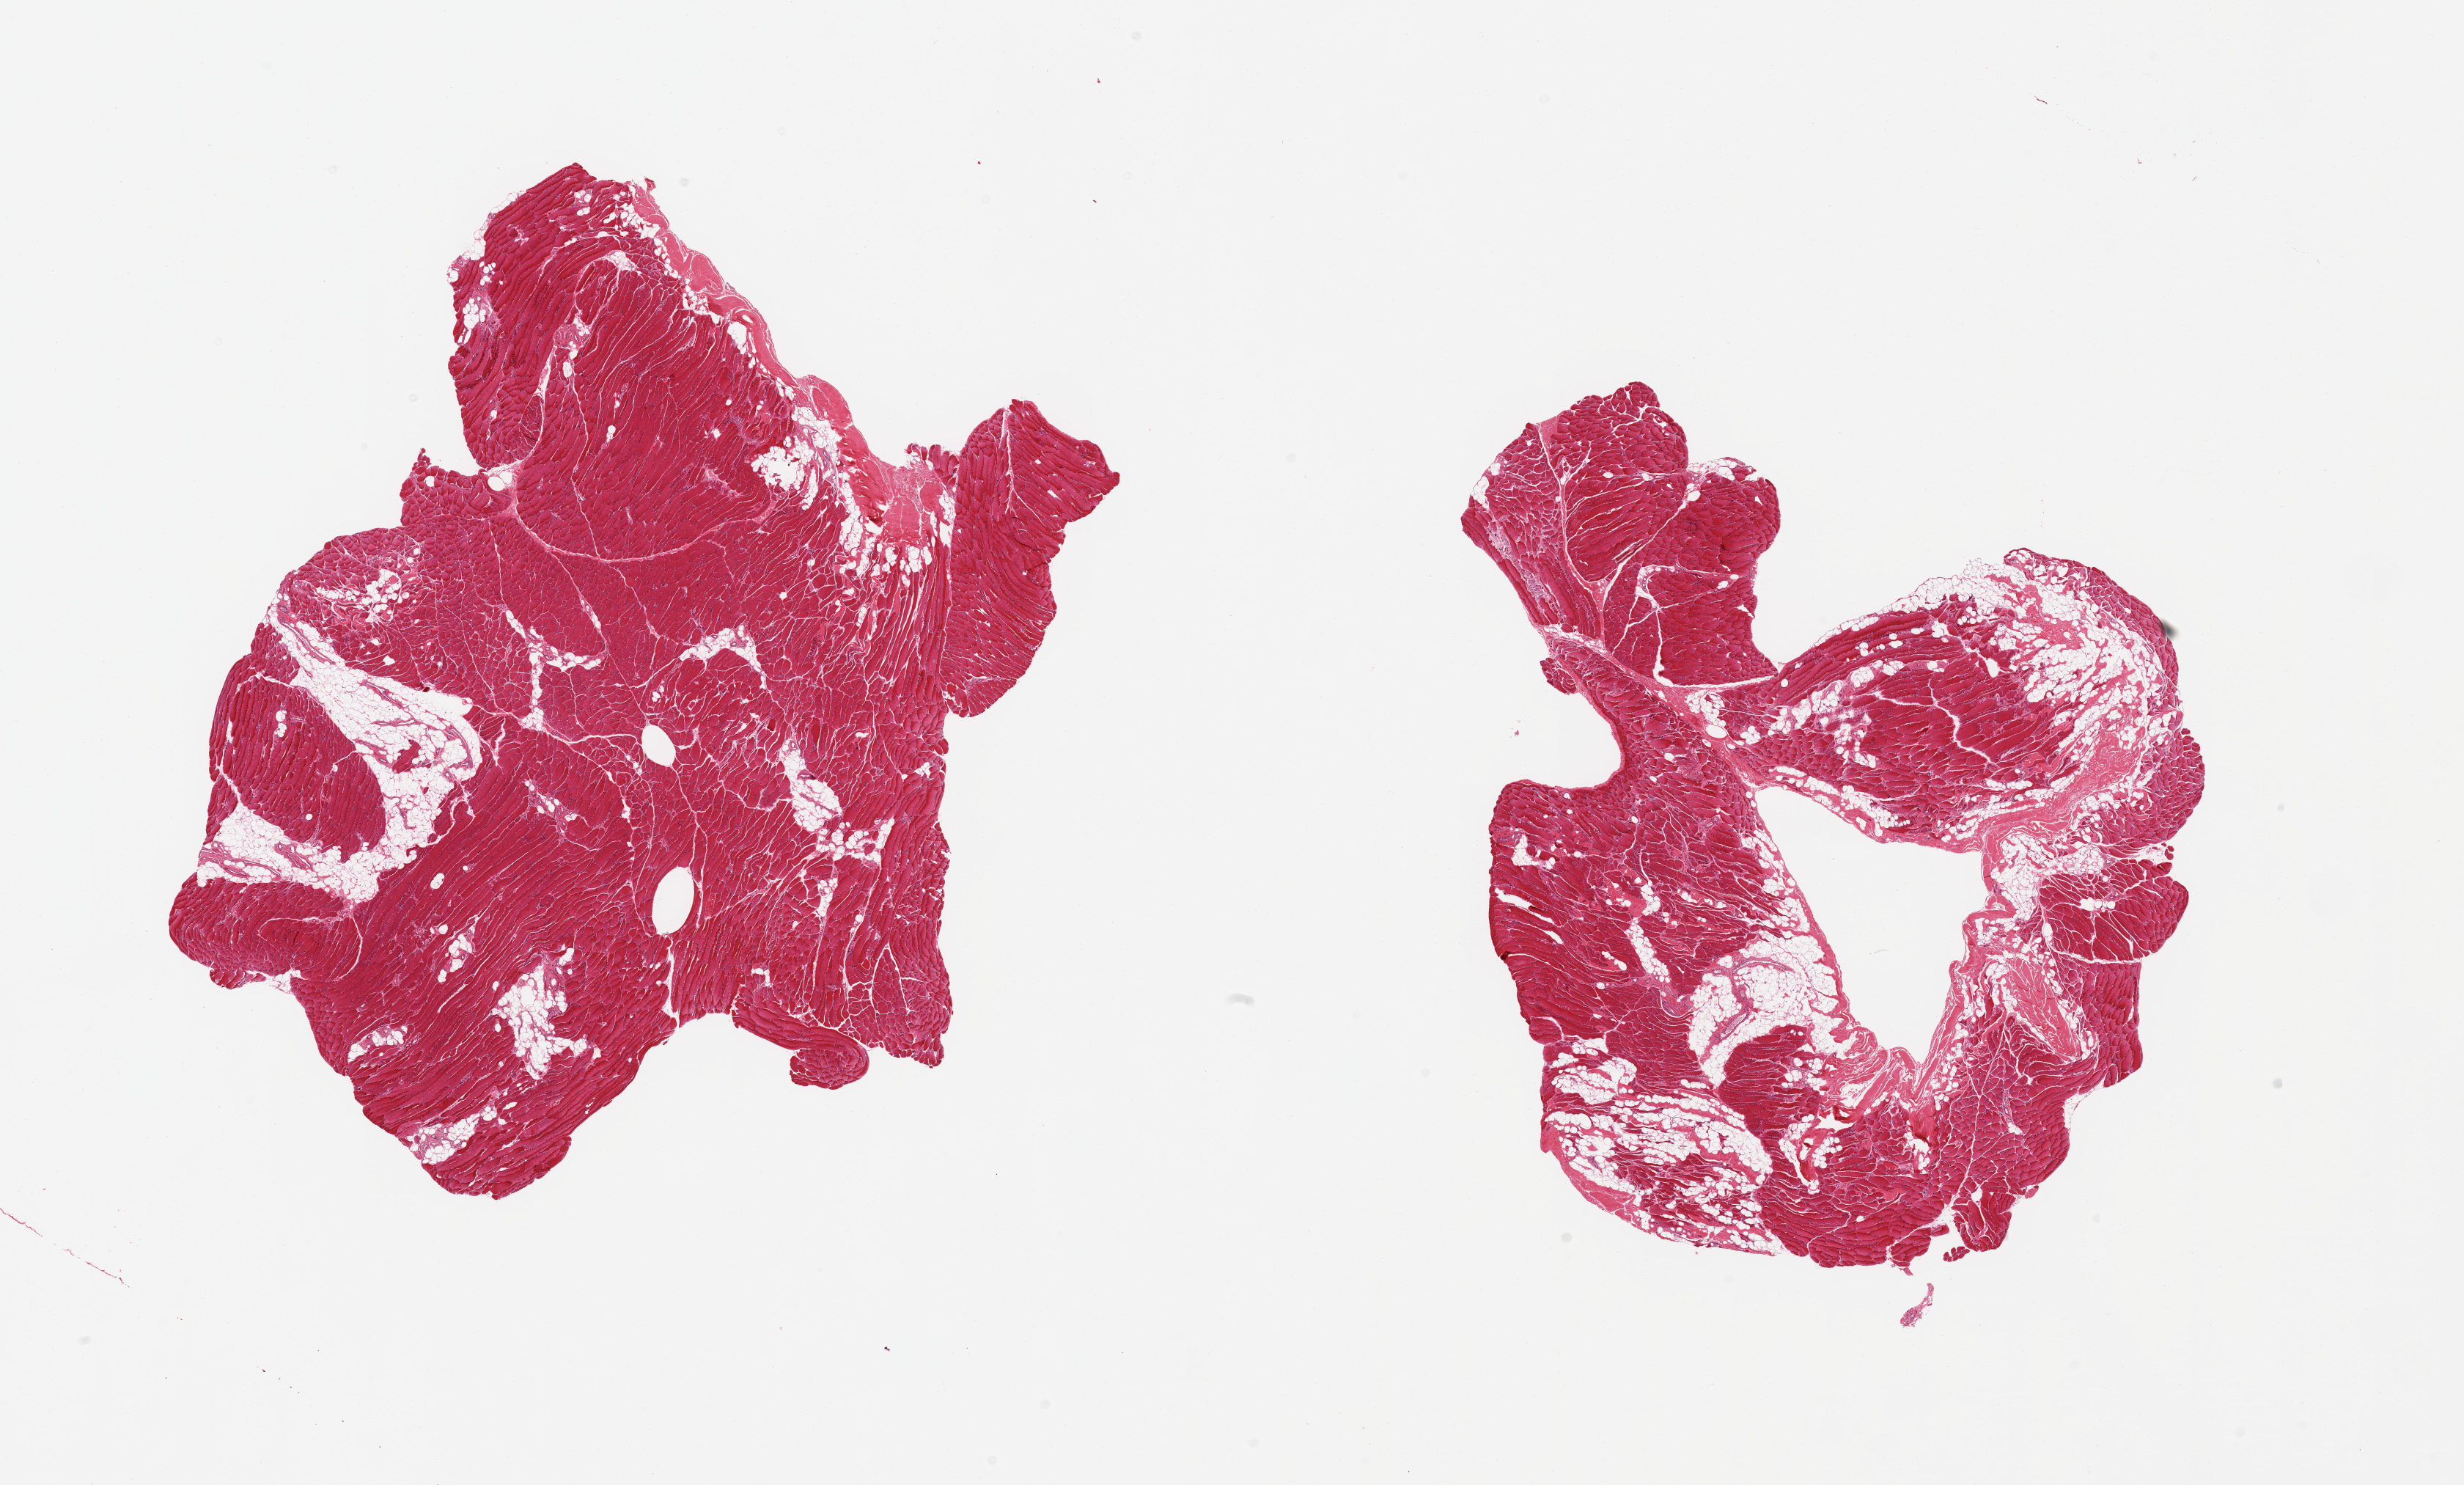
Whole-slide image, hematoxylin and eosin (H&E) stain, brightfield — a low-resolution overview of the entire scanned area, about 26.6 x 16.0 mm, PAXgene-fixed paraffin-embedded (PFPE) section, section of skeletal muscle (target tissue), donor tissue sample. Donor: male.
* pathologist's review note for this sample: 2 pieces; 40 & 10% internal fat